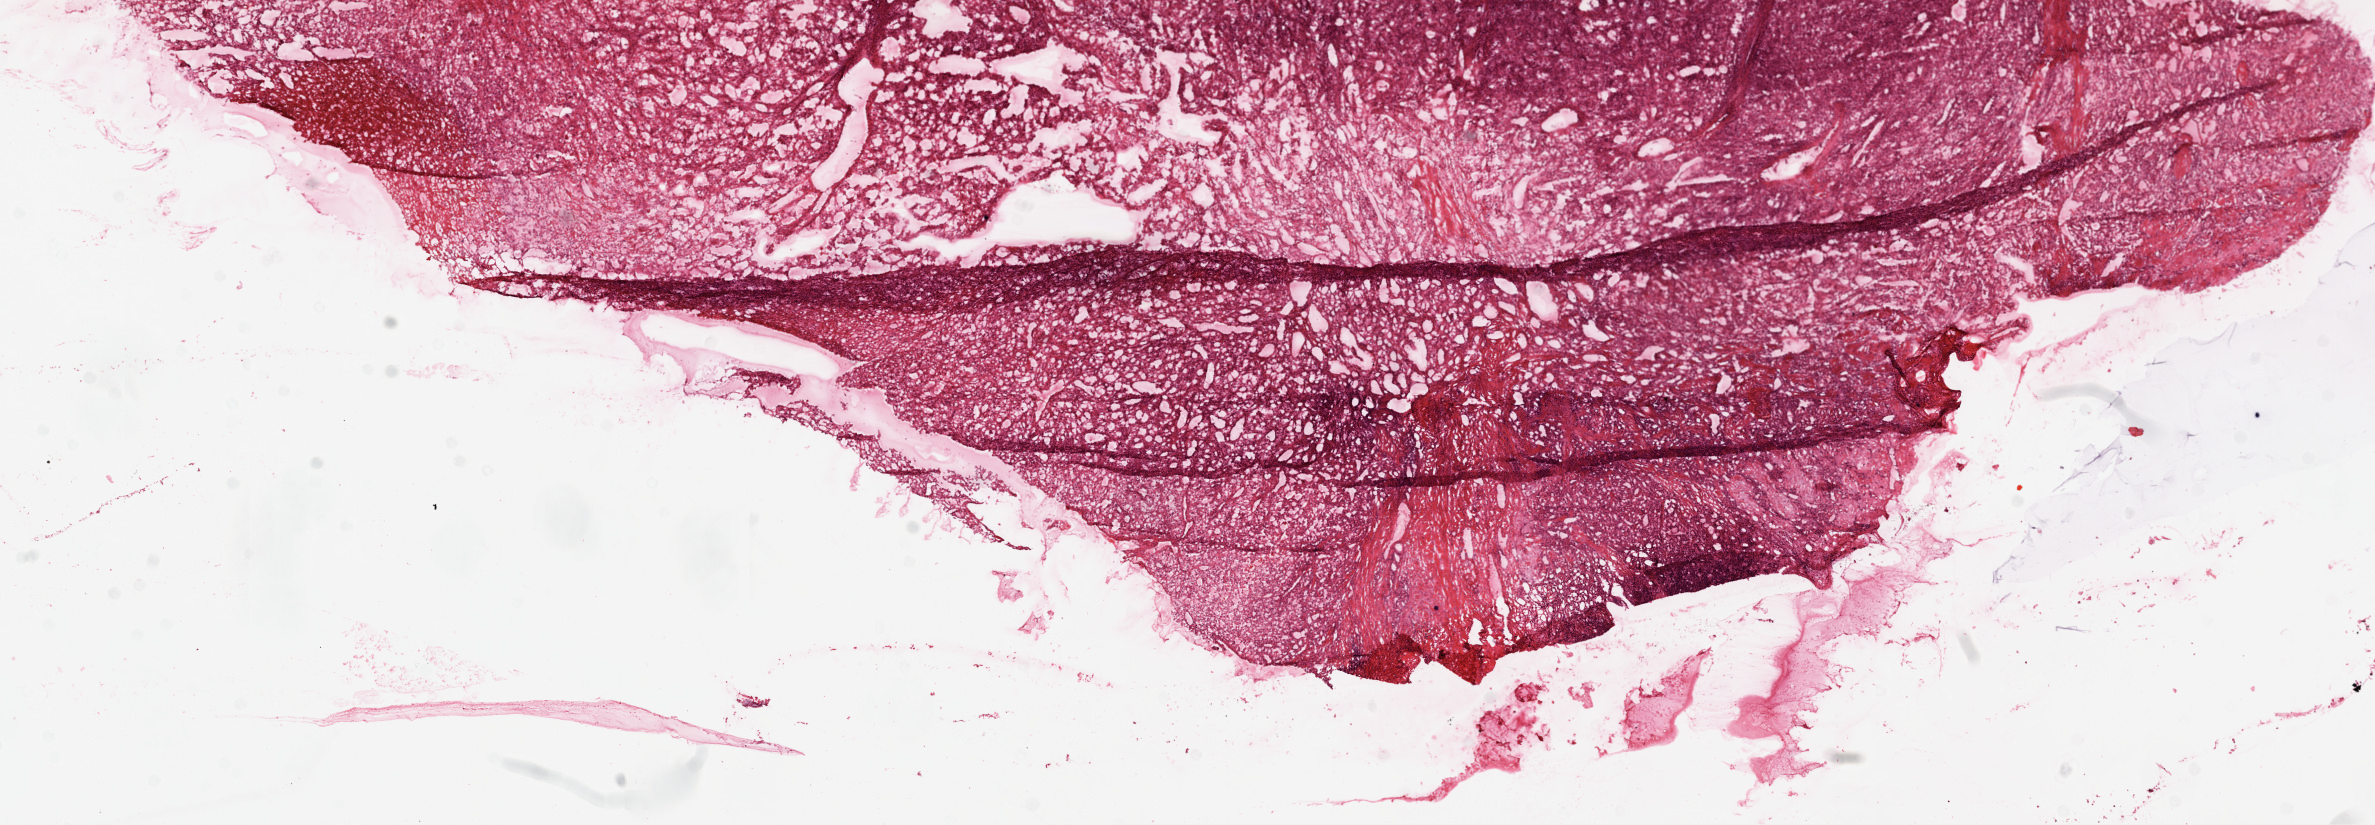
Digitized H&E tissue section (whole slide), a low-resolution overview of the entire scanned area, about 19.1 x 6.6 mm, frozen section, sample: primary tumour, kidney. Patient: male, age at initial diagnosis 78 years. Histologic grade: G4 (undifferentiated). Slide review estimates, as recorded: tumour cells 90%, tumour nuclei 90%, normal cells 0%, stromal cells 10%, necrosis 0%.
* diagnosis: Clear cell adenocarcinoma, NOS
* AJCC pathologic stage: II